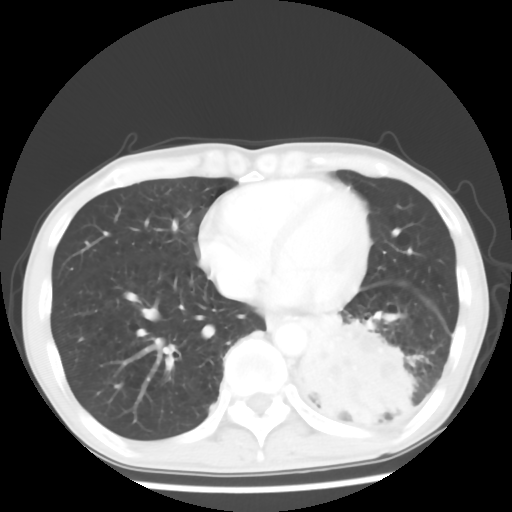
Chest CT, one axial slice. Slice 21 of 64 in the series (ordered by position). Reconstruction kernel STANDARD. 120 kVp. Lung window (W 1500 / L -600 HU). 512 × 512 image matrix. Patient: male, 68 years. From the clinical record (not read from this slice): clinical TNM (as recorded): T4 N0 M0.
Structures marked on this image (rectangle marked by the reading radiologist):
- lung tumour (recorded histology: squamous cell carcinoma): bounding box (x1, y1, x2, y2) in pixels: (295, 292, 427, 426)